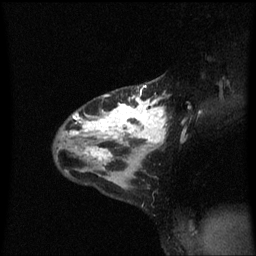
Breast MRI (dynamic contrast-enhanced), one sagittal slice; position 40 of 60 along the scan axis; dynamic contrast-enhanced series, image 2 of 3 at this slice position (ordered by acquisition); 1.5 T; TE 4.2 ms, TR 8.4 ms; 256 × 256 image matrix, field of view 200 × 200 mm. Female patient, age 32 years.
Outlined on this slice (semi-automatic segmentation, software-assisted and operator-edited):
- analysis volume of interest (the breast-tissue region the enhancement analysis was run in; not a lesion): box from (x=55, y=78) to (x=170, y=167) px
- tumour enhancement mask (voxels above the 70 % enhancement threshold inside the analysis volume of interest): (x=66, y=86)–(x=168, y=163)